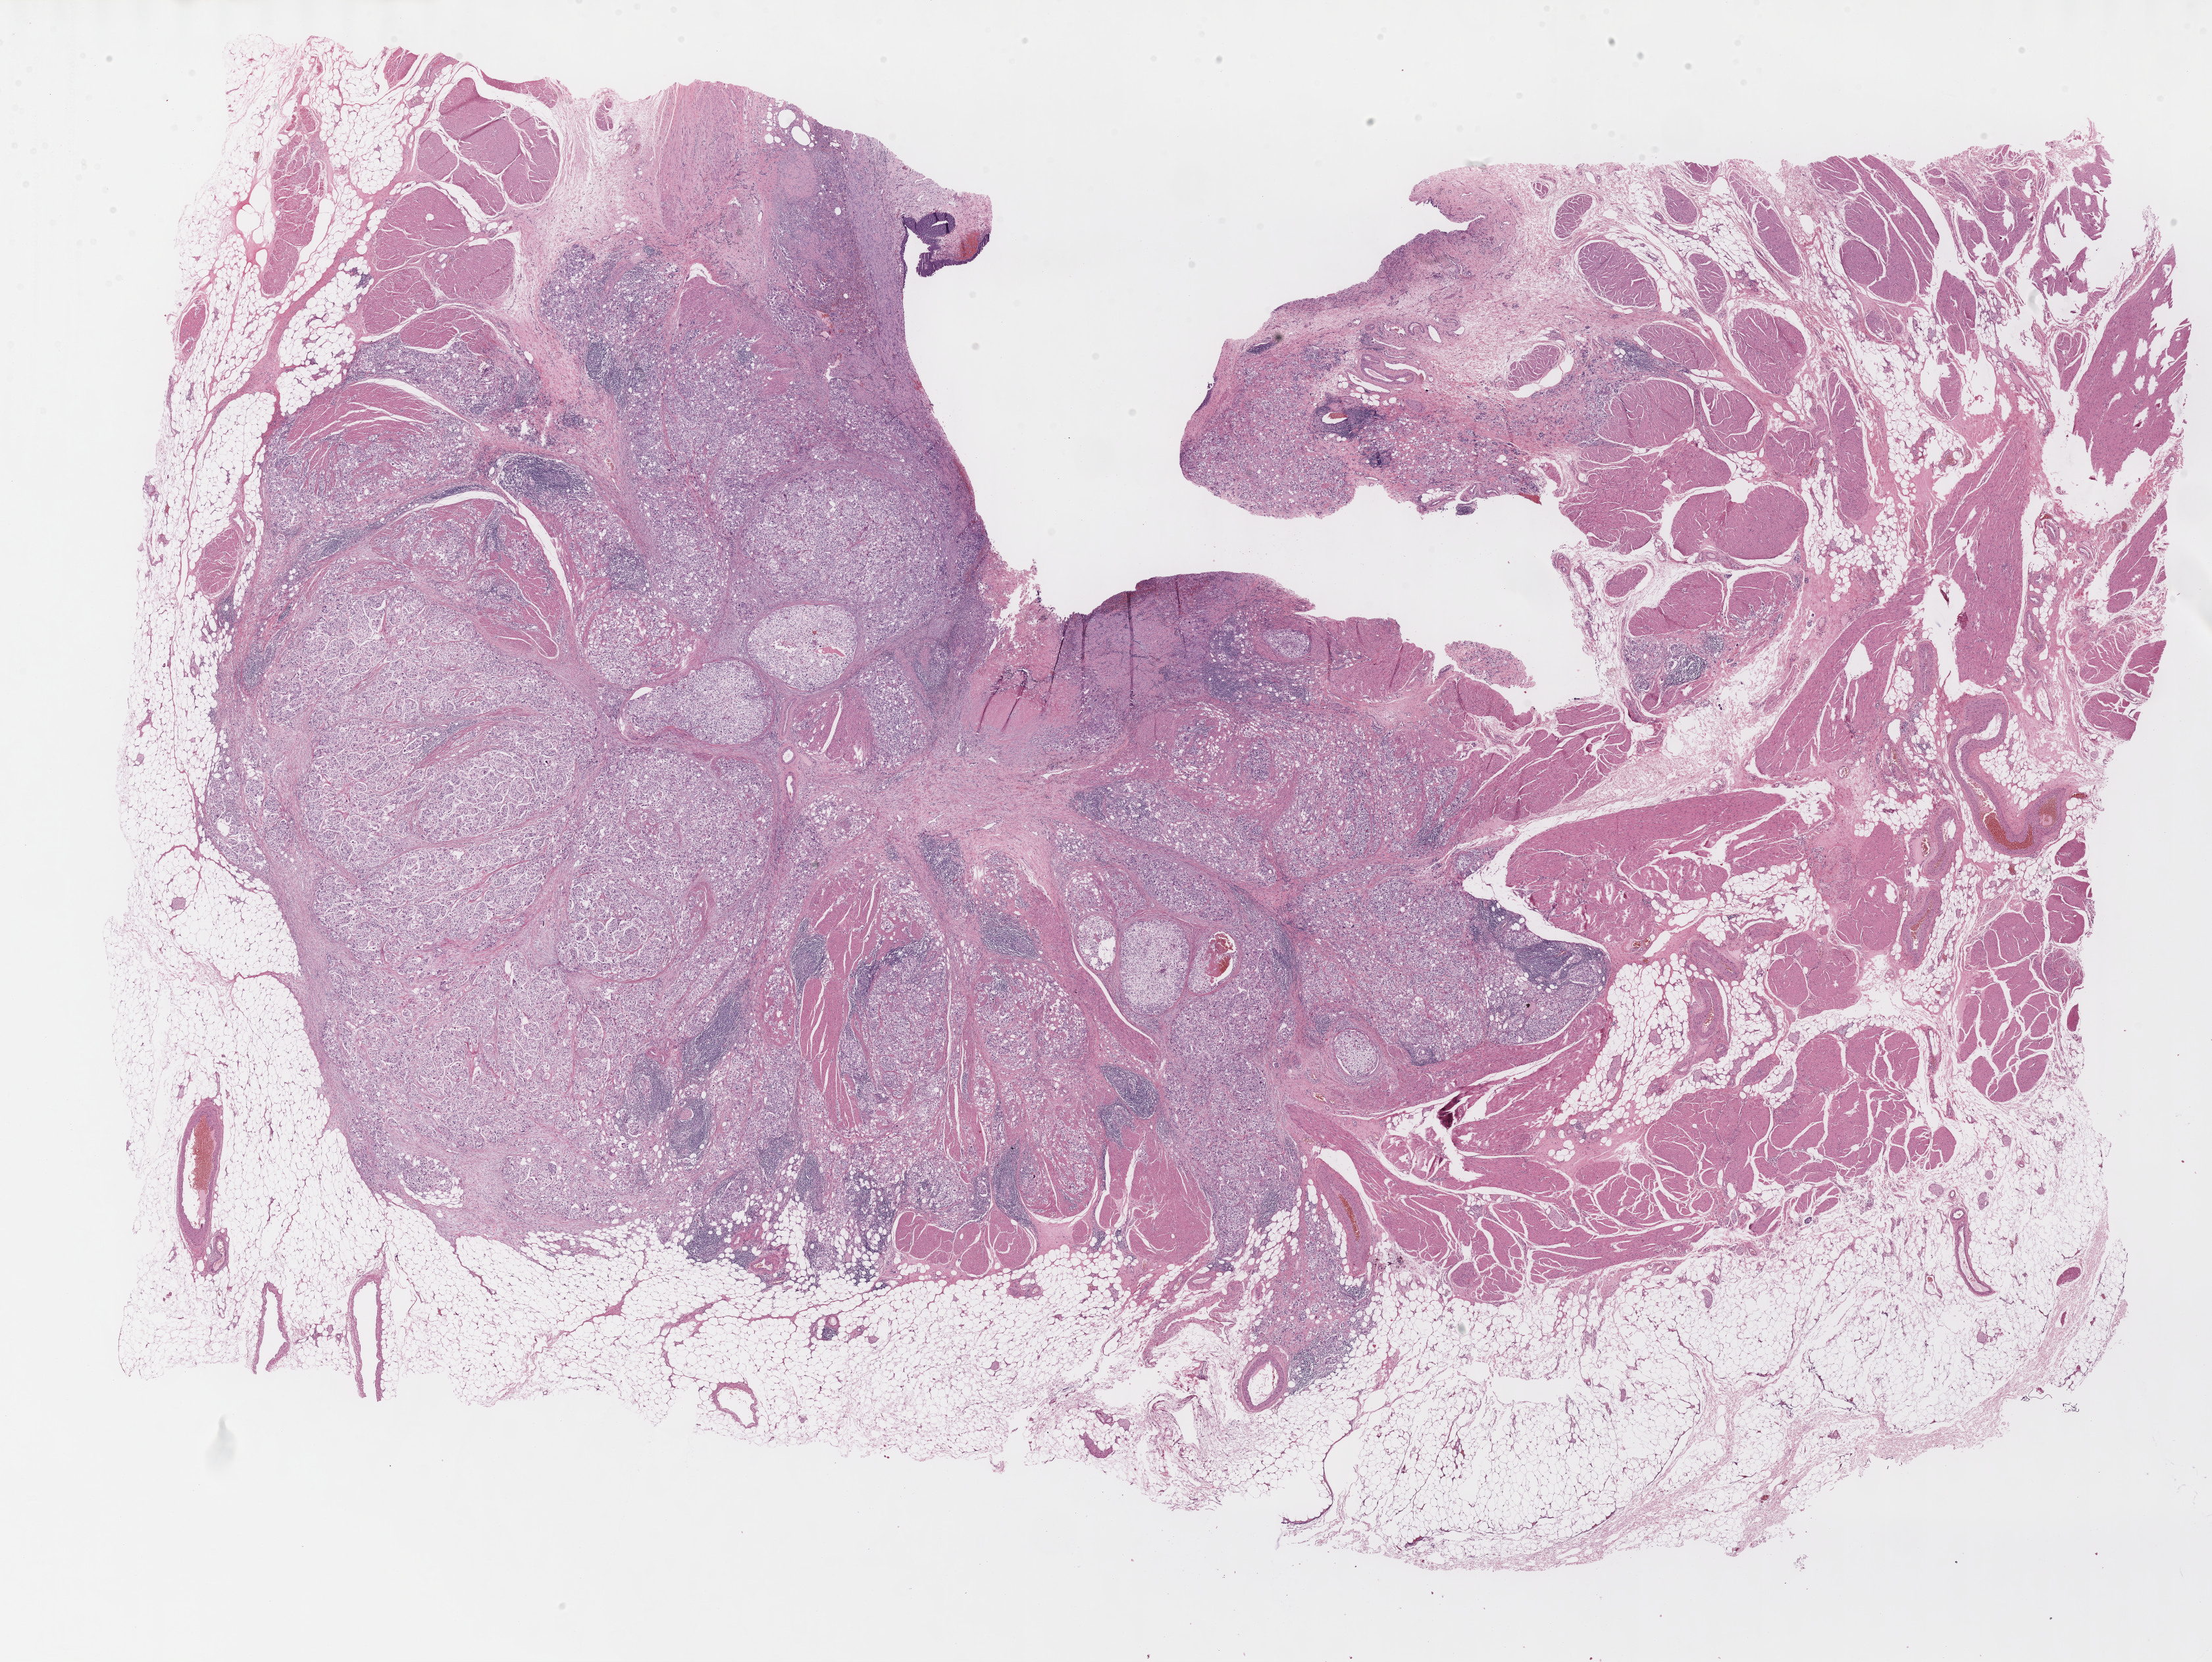
Whole-slide histology image, Hematoxylin and eosin (H&E) stained, whole scanned area (about 27.2 x 20.4 mm) shown as a low-resolution overview; formalin-fixed paraffin-embedded (FFPE) diagnostic section; bladder, primary tumour sample. Male patient; age at initial diagnosis 65 years. Histologic grade: high grade.
AJCC pathologic stage: III. Histologic diagnosis: Transitional cell carcinoma (lateral wall of bladder). Lymph nodes positive (case pathology): 0 of 23 examined.